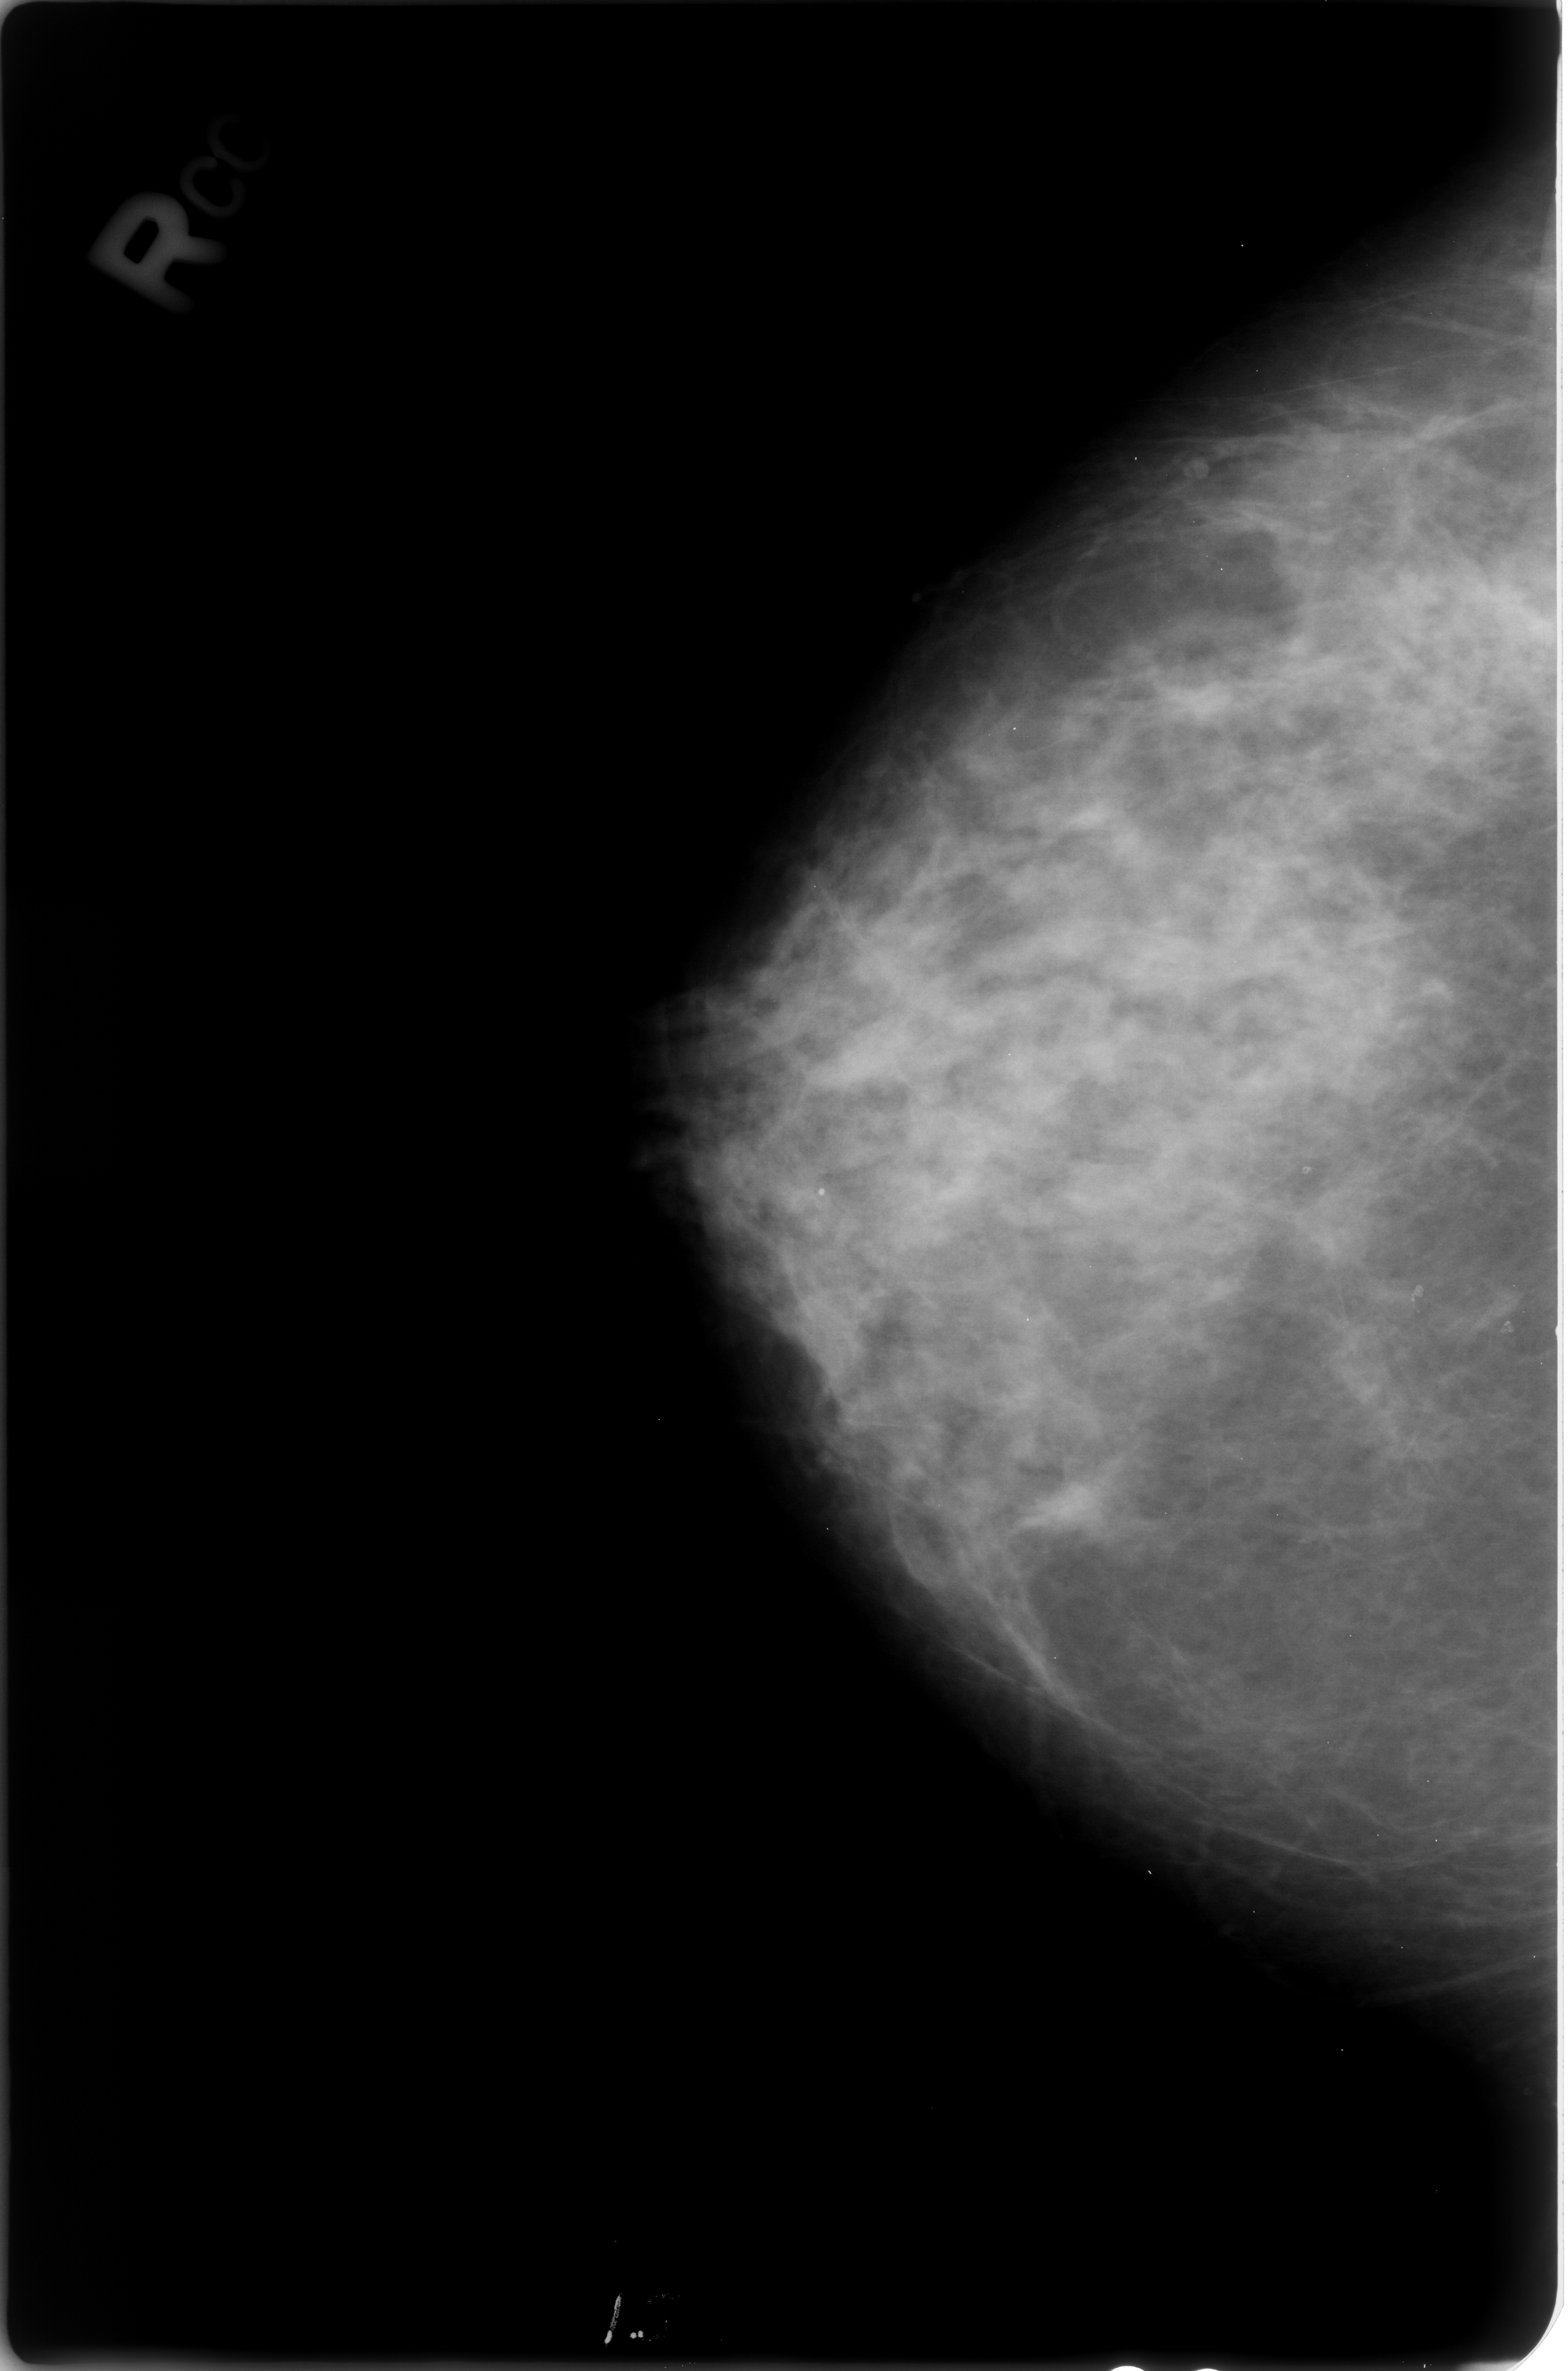
Scanned film-screen mammogram, right breast, craniocaudal (CC) view, breast composition: heterogeneously dense (BI-RADS density category 3 of 4).
Abnormality record for this image: Finding 1 of 2: calcifications, morphology round and regular / lucent center; BI-RADS assessment category 2; subtlety rating 3 on a 1 (subtle) to 5 (obvious) scale; benign; no additional work-up was recommended (benign without callback). Finding 2 of 2: calcifications, morphology round and regular / lucent center; BI-RADS assessment category 2; subtlety rating 3 on a 1 (subtle) to 5 (obvious) scale; benign without callback (not worked up further).